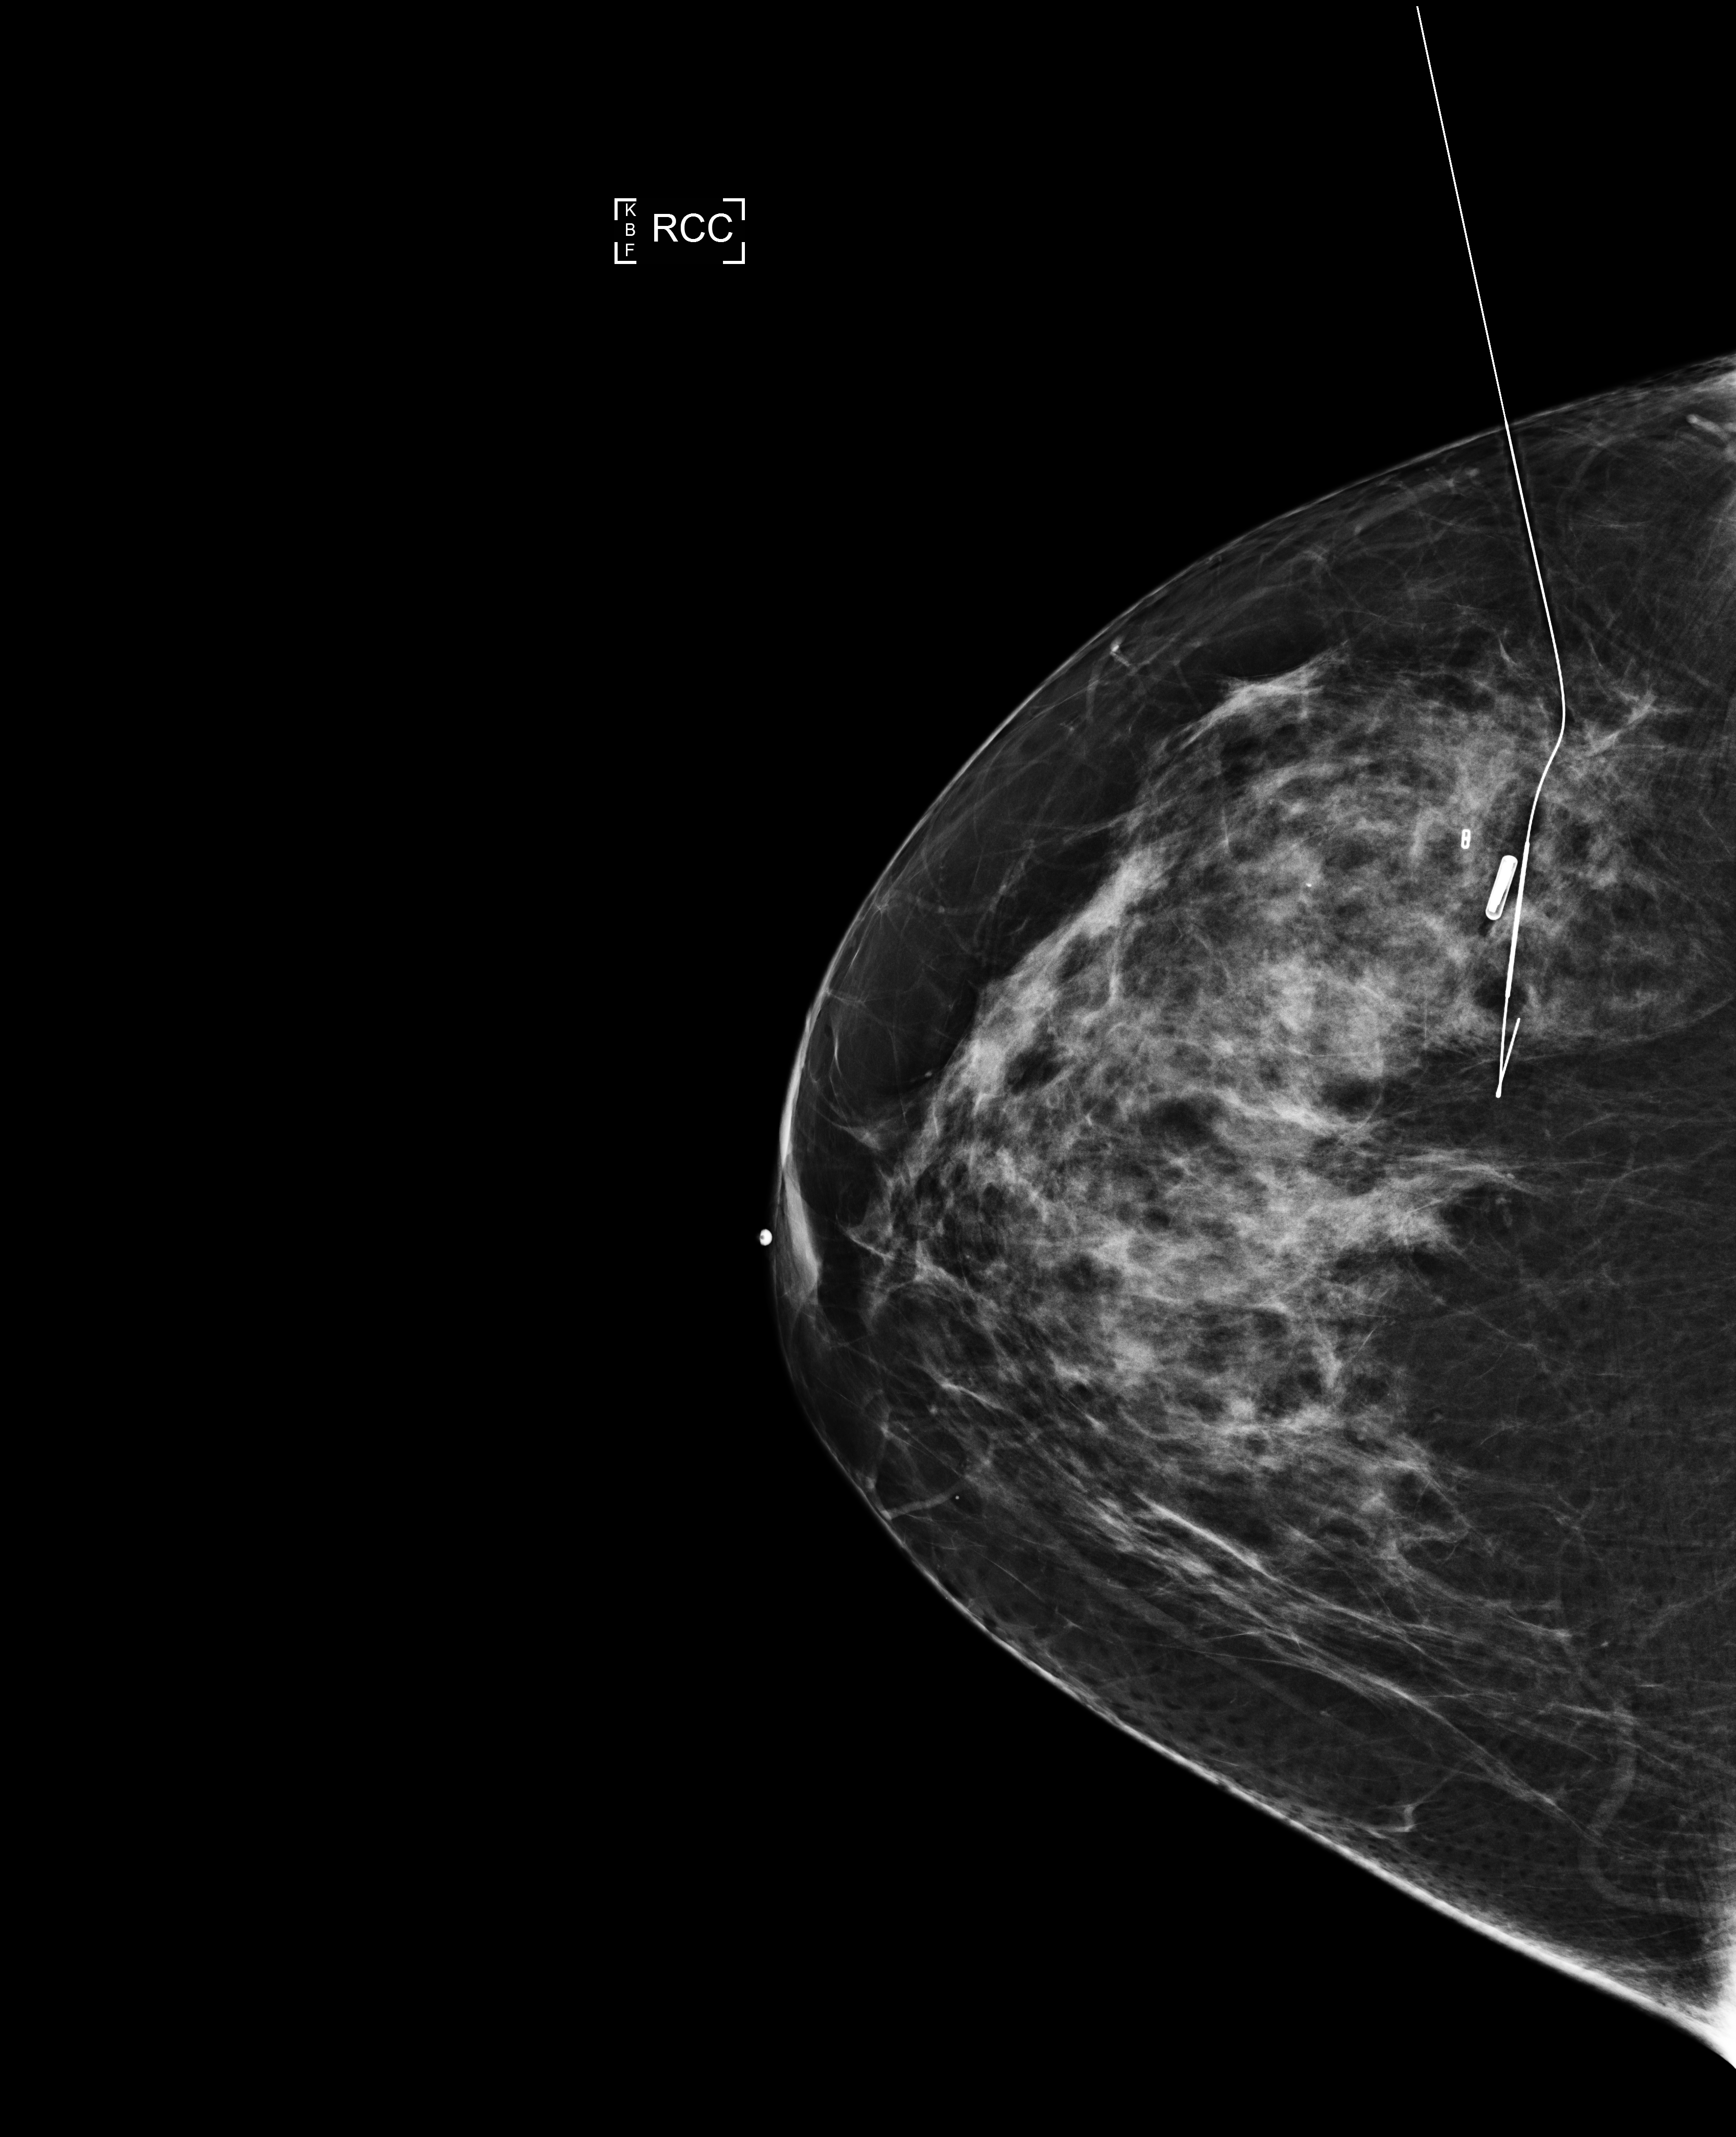
Diagnostic examination (additional views), compressed breast thickness 73 mm, system: Selenia Dimensions. Patient: female, 50 years.
Image type: full-field digital mammogram. Breast: right. Projection: craniocaudal (CC) view.